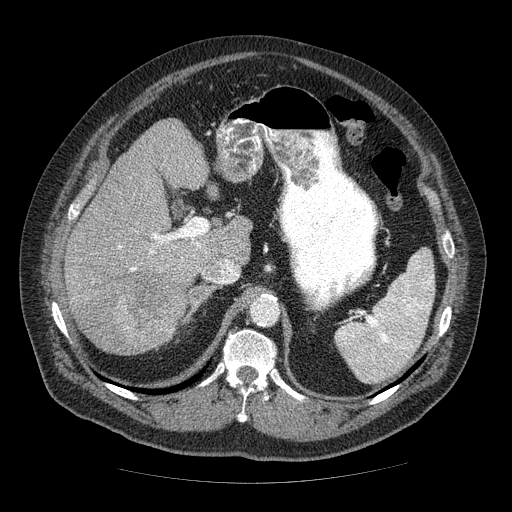
Contrast-enhanced abdominal CT (liver protocol), one axial slice. Slice 35 of 85 in the series (ordered by position). Soft-tissue window (W 400 / L 40 HU). 2.5 mm slice thickness. 512 × 512 image matrix. Case-level facts recorded for this patient, not image findings: diagnosis: hepatocellular carcinoma (patient treated with transarterial chemoembolisation; whether this scan precedes or follows treatment is not stated here); TNM stage (as recorded): Stage-IIIA; Child-Pugh class: A; tumour nodularity: multinodular.
Outlined on this slice (semi-automatic segmentation, software-assisted and operator-edited):
- liver parenchyma outside the tumour (the mass and vessels are separate outlines, so this box may not span the whole liver): bounding box [x1, y1, x2, y2] px = [64, 120, 252, 342]
- mass: [71, 264, 186, 356]
- liver vessels: [92, 232, 230, 283]